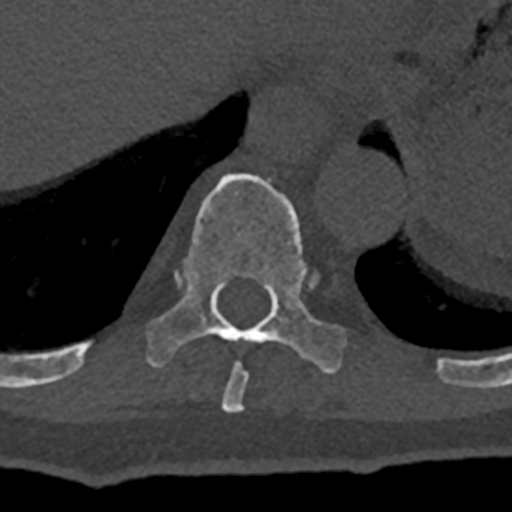
CT including the spine, one axial slice; slice 609 of 797 in the series (ordered by position); reconstruction kernel Br40s/3; 120 kVp; bone window (W 1800 / L 400 HU); 512 × 512 image matrix, field of view 160 × 160 mm. Male patient, age 74 years. From the clinical record (not read from this slice): primary cancer: renal; vertebrae with lytic lesions (as recorded): T10, L1, L2, L3, L4, L5.
Outlined on this slice (semi-automatic segmentation, software-assisted and operator-edited):
- T10 vertebra: bounding box [x1, y1, x2, y2] px = [70, 173, 346, 374]
- T9 vertebra: [221, 362, 248, 413]